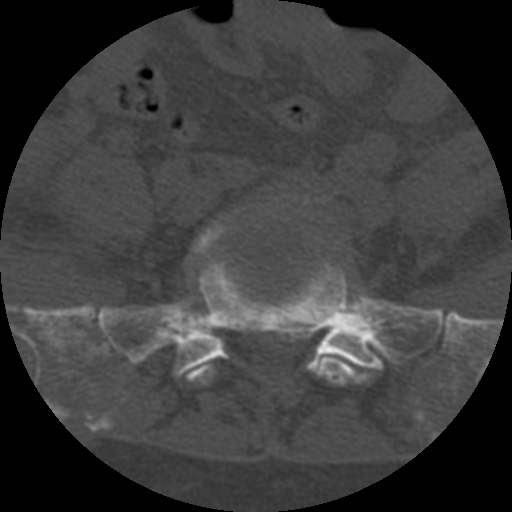
CT including the spine, one axial slice. 120 kVp. One of 3 acquisitions stored at this slice position. Bone window (W 1800 / L 400 HU). 512 × 512 image matrix, field of view 160 × 160 mm. Patient age 55 years. From the clinical record (not read from this slice): primary cancer: colon; vertebrae with lytic lesions (as recorded): T12, L1, L5.
Annotated regions visible in this slice (semi-automatic segmentation, software-assisted and operator-edited):
- L5 vertebra: box from (x=187, y=222) to (x=371, y=385) px